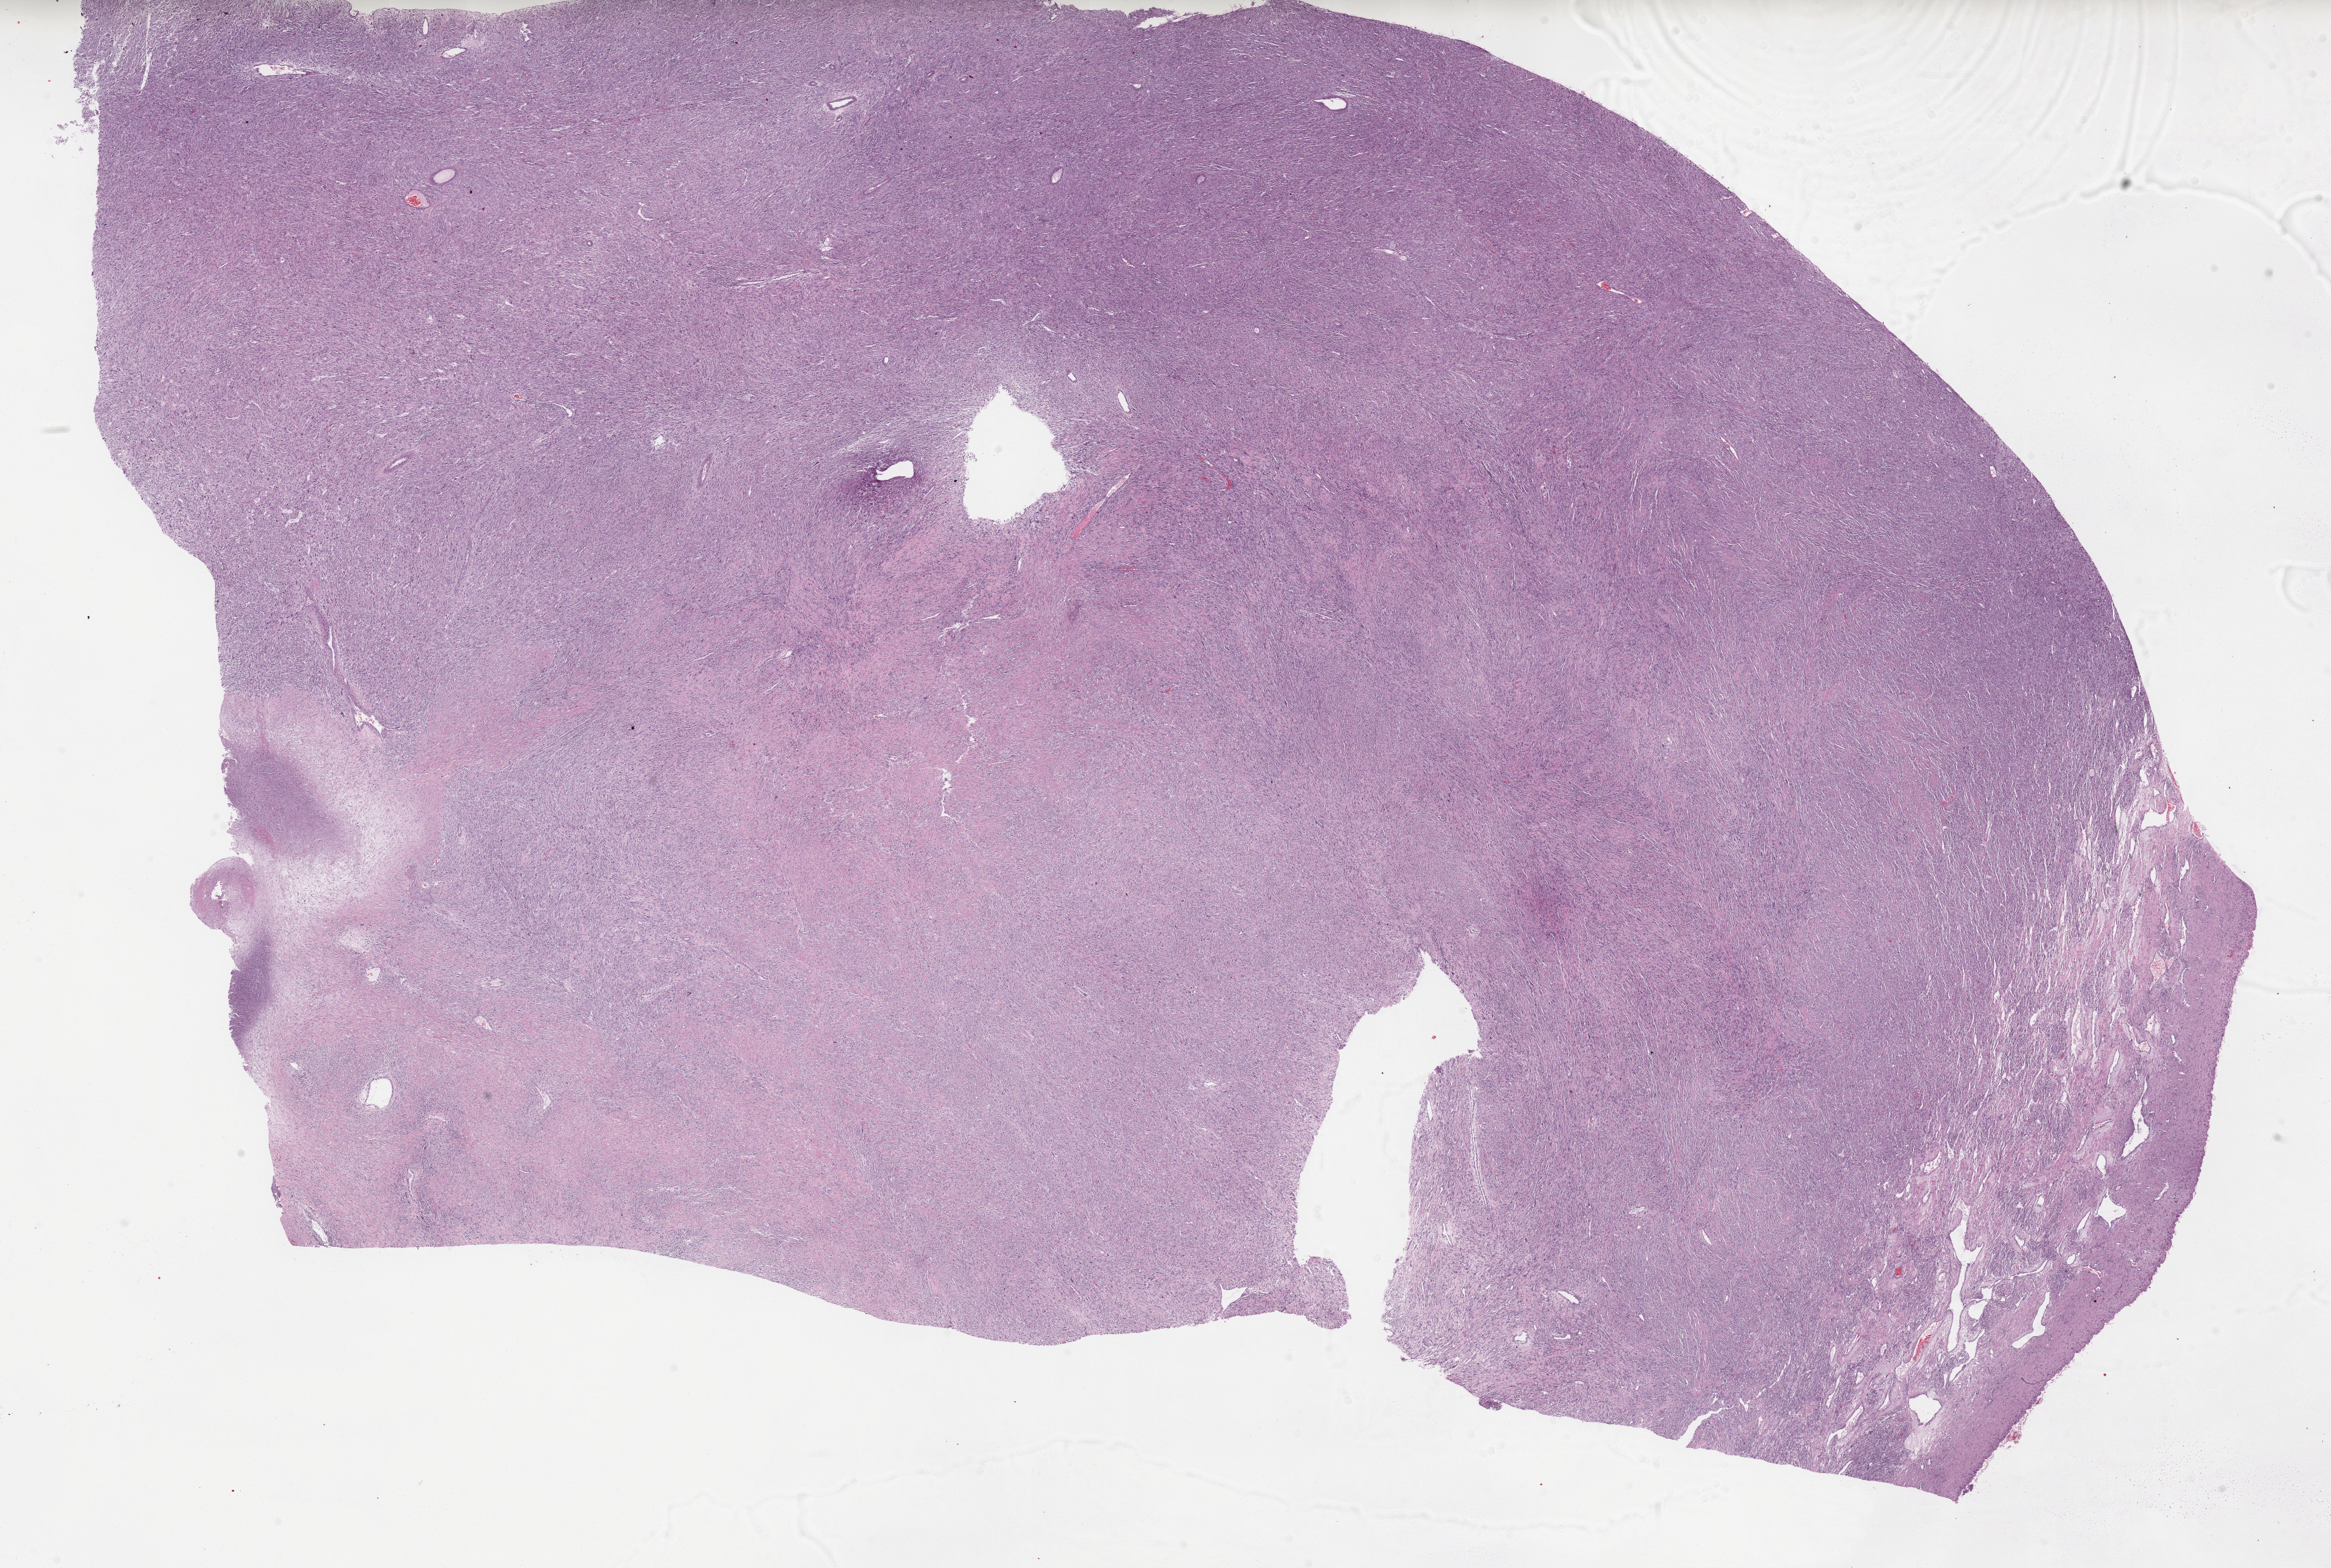
H&E-stained whole-slide image, low-resolution overview of the scanned area, about 29.7 x 20.0 mm (from a 20x scan). Formalin-fixed paraffin-embedded (FFPE) diagnostic section. Retroperitoneum and peritoneum, primary tumour sample. Male, age 51 years at initial diagnosis.
Histologic diagnosis: Dedifferentiated liposarcoma.